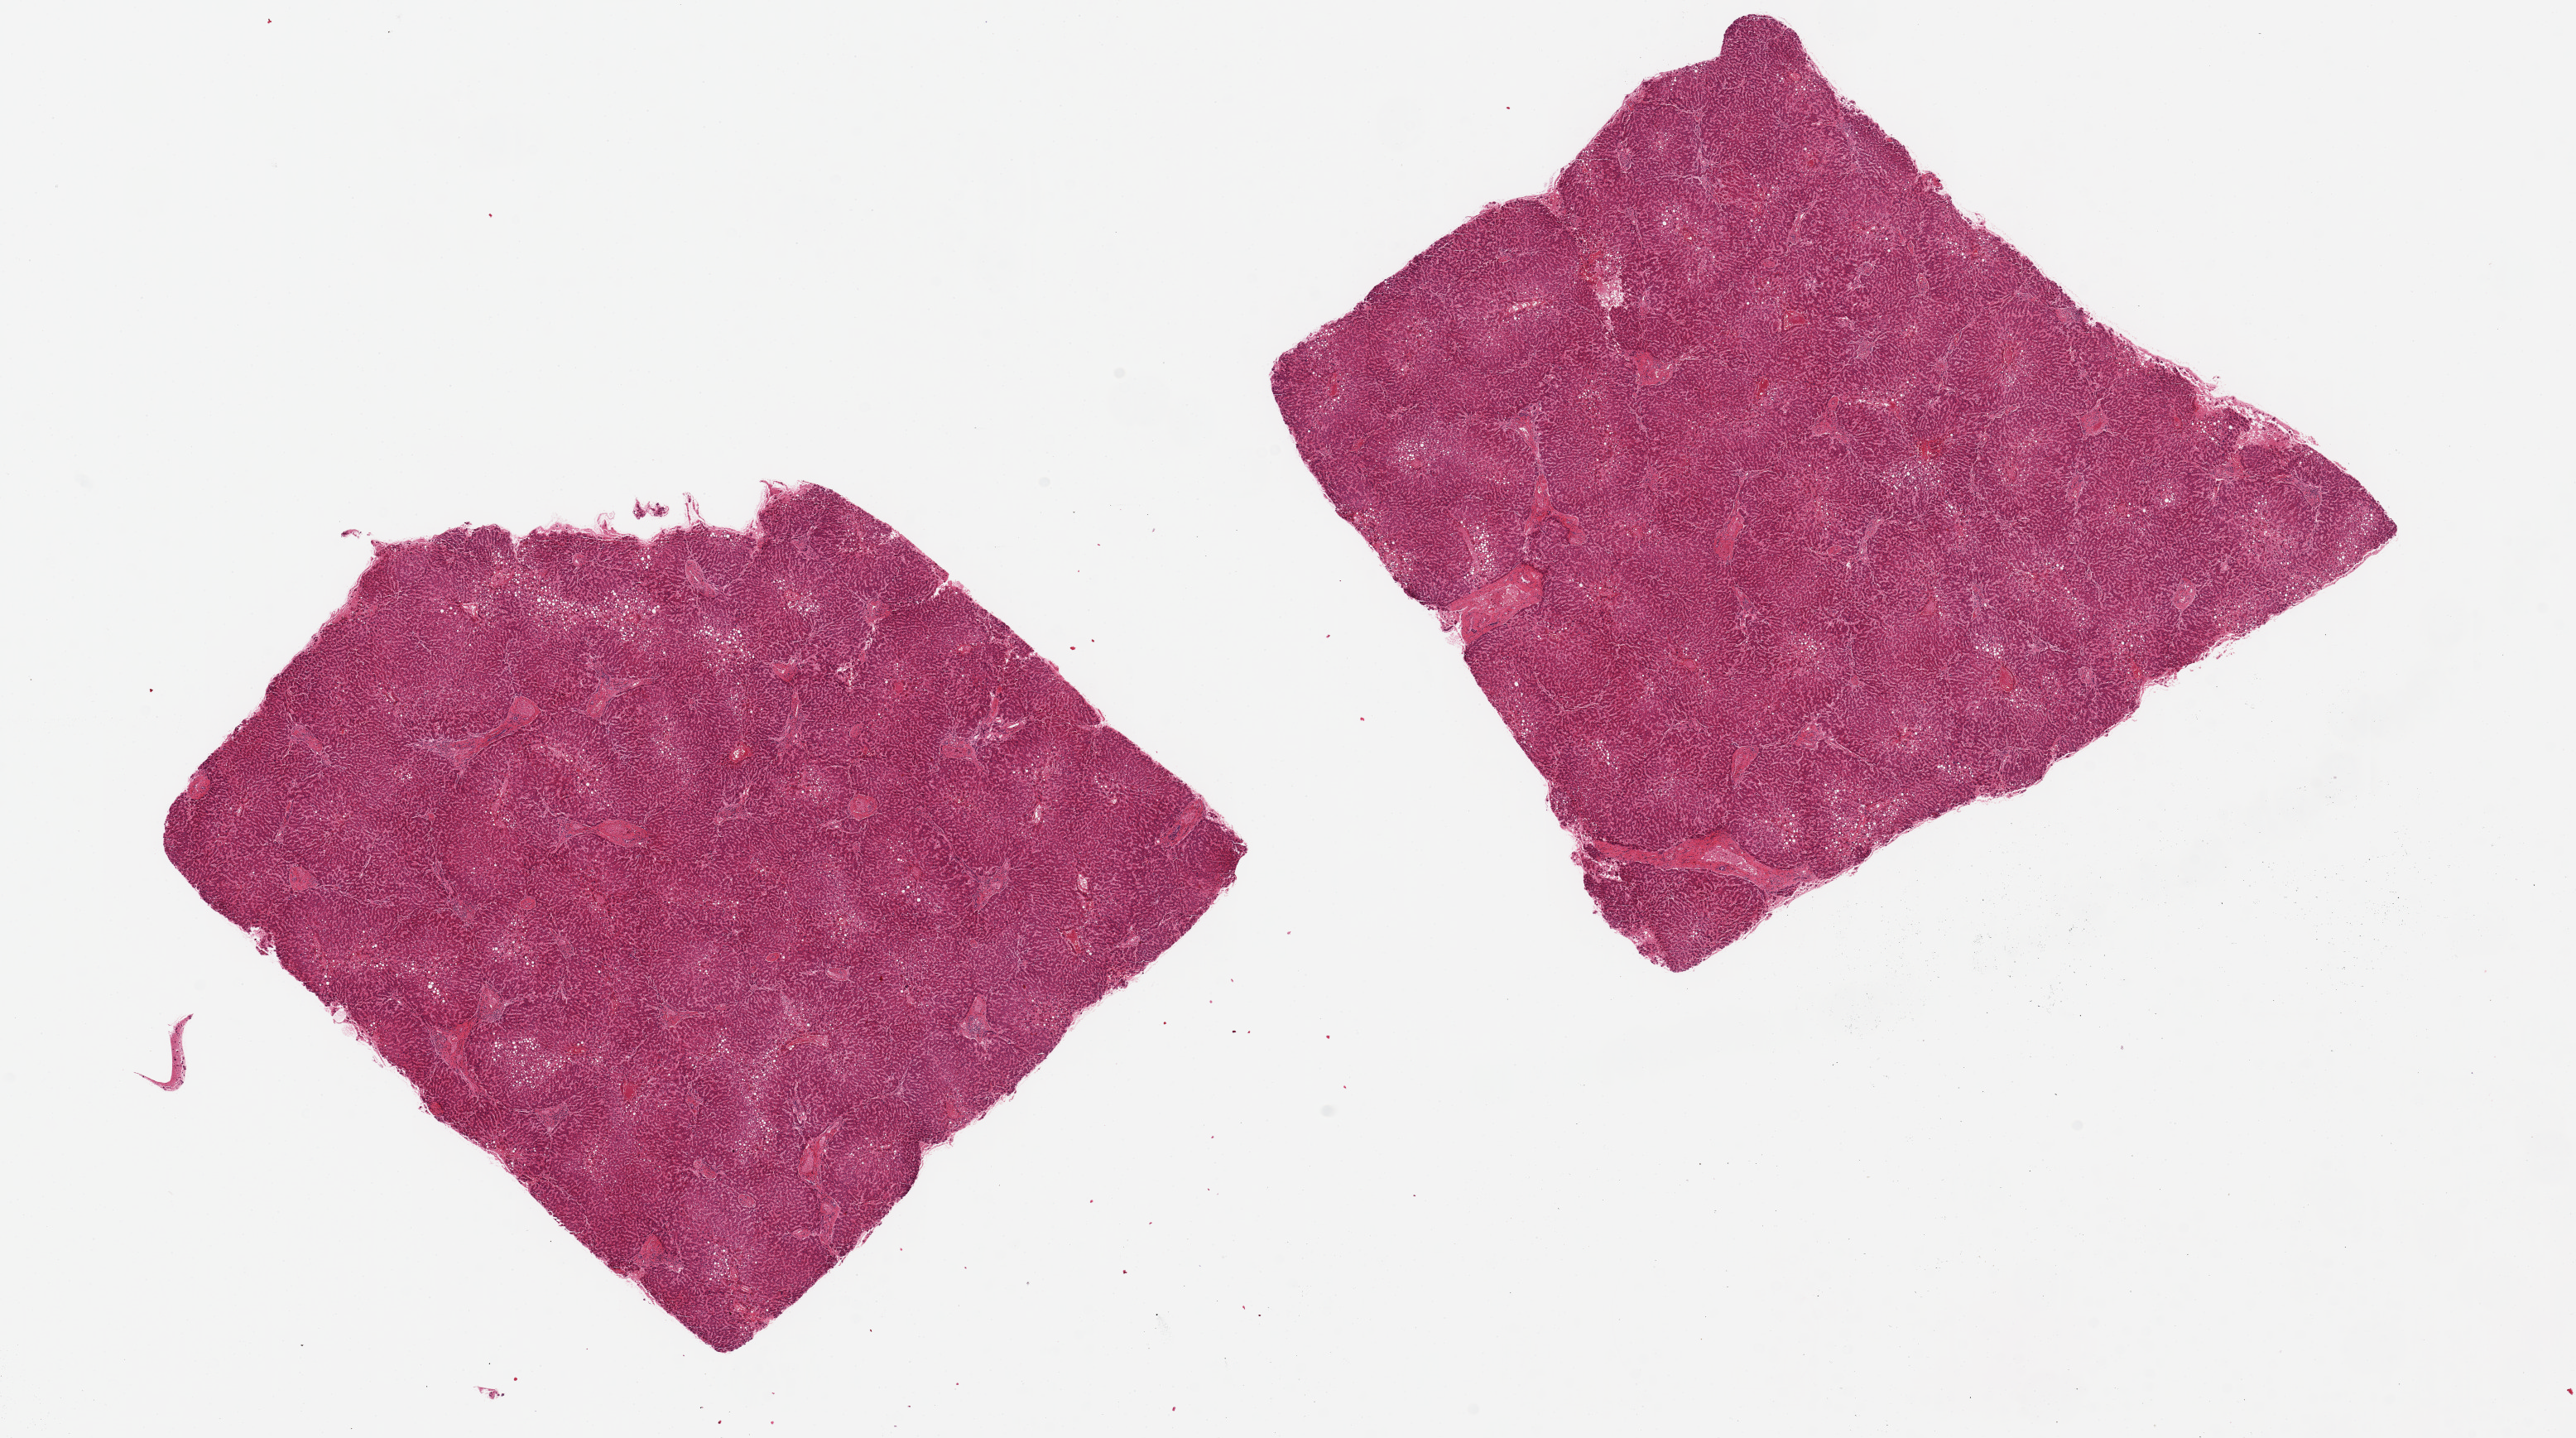
H&E whole-slide image, brightfield — a low-resolution overview of the entire scanned area, about 24.6 x 13.7 mm (acquisition: 20x scan); PAXgene-fixed paraffin-embedded (PFPE) section; target tissue: liver; tissue donor sample. Donor sex: male.
• pathologist's review note for this sample: 2 pieces, 8x7 & 8x8mm; 20% macrovesicular steatosis